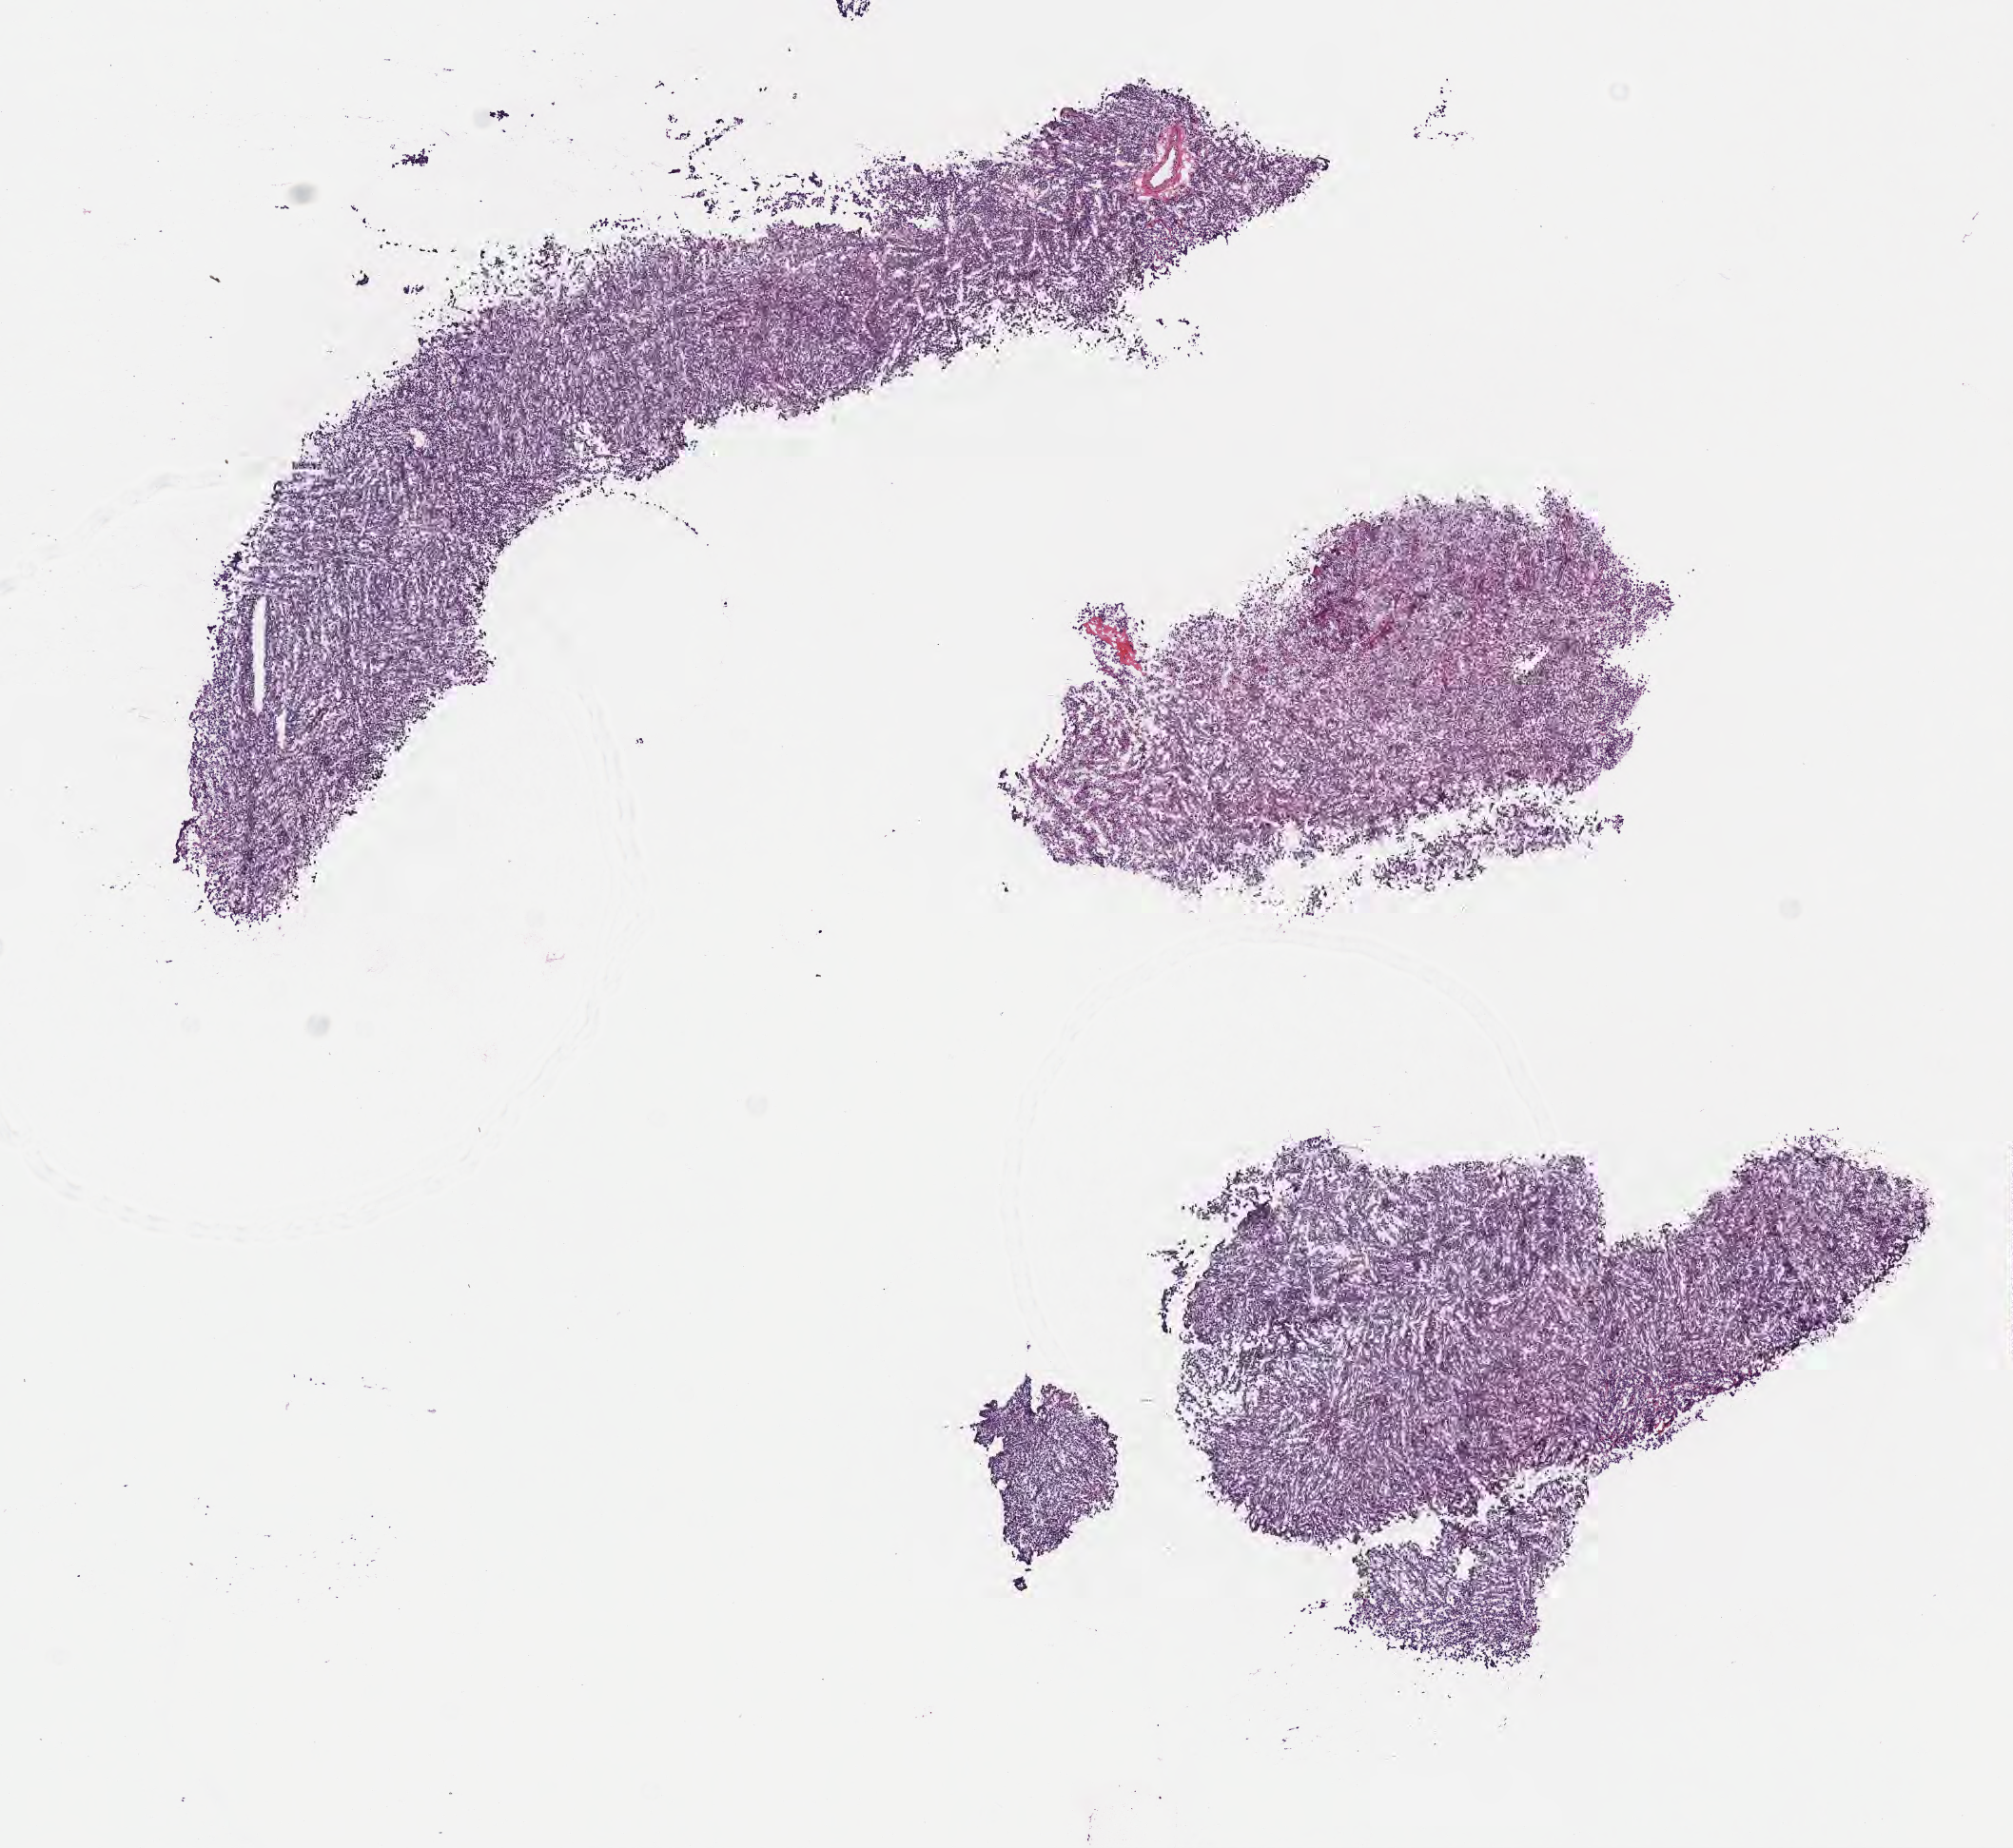
Whole-slide image, H&E stain, low-resolution overview of the scanned area, about 8.6 x 7.9 mm, frozen section (tissue freezing medium), primary tumor, site: spleen. Male patient; age at initial diagnosis 8 years.
Diagnosis: Burkitt lymphoma, NOS.